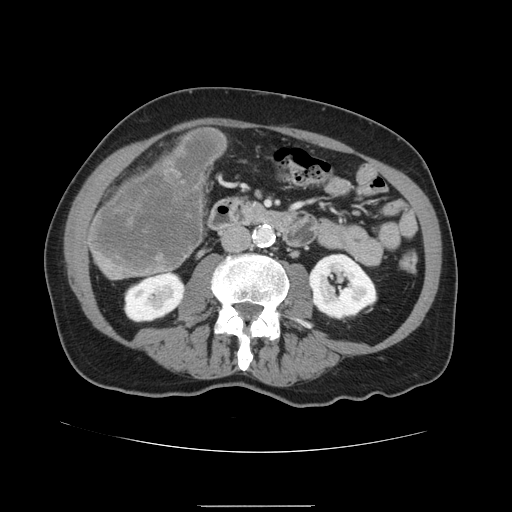
Contrast-enhanced abdominal CT, one axial slice. Slice 36 of 168 in the series (ordered by position). 120 kVp. Intravenous contrast given. Soft-tissue window (W 400 / L 40 HU). 2.5 mm slice thickness. 512 × 512 image matrix, field of view 386 × 386 mm. Male patient, age 74 years. Case-level facts recorded for this patient, not image findings: diagnosis: colorectal cancer liver metastases, imaged before liver resection; multiple liver metastases: no; largest metastasis: 14.5 cm.
Outlined on this slice (expert manual segmentation):
- liver: bounding box <88,128,227,280> (left, top, right, bottom; pixels)
- liver metastasis: <91,131,224,274>